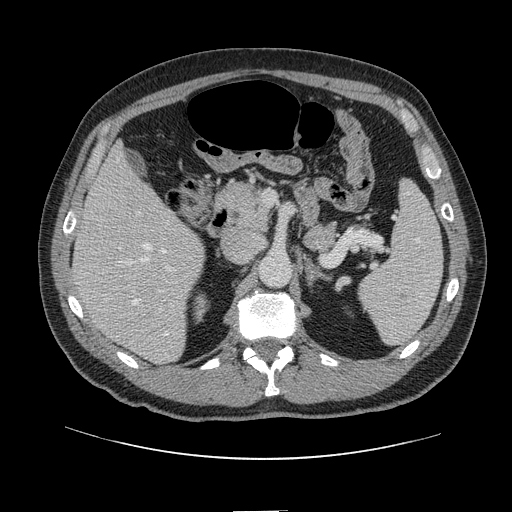
Contrast-enhanced abdominal CT, one axial slice. Slice 67 of 161 in the series (ordered by position). Intravenous contrast given. Soft-tissue window (W 400 / L 40 HU). 512 × 512 image matrix, field of view 412 × 412 mm. Male patient, age 66 years. Case-level facts recorded for this patient, not image findings: diagnosis: colorectal cancer liver metastases, imaged before liver resection; multiple liver metastases: no; largest metastasis: 3.5 cm; disease in both lobes: no.
Outlined on this slice (outlined manually by an expert reader):
- hepatic veins: bounding box <118,159,168,335> (left, top, right, bottom; pixels)
- liver: <75,149,204,363>
- planned liver remnant (the part of the liver to remain after resection): <75,149,180,288>
- portal vein (with intrahepatic branches): <119,212,177,314>